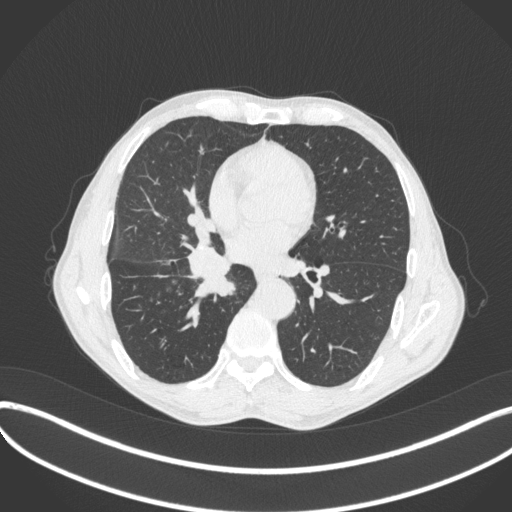
Chest CT, one axial slice. Slice 204 of 481 in the series (ordered by position). Reconstruction kernel B31f. 120 kVp. Lung window (W 1500 / L -600 HU). 1 mm slice thickness. 512 × 512 image matrix, field of view 400 × 400 mm. Patient: male, 65 years. Case-level facts recorded for this patient, not image findings: clinical TNM (as recorded): T2a N0 M0; histopathological grade: G2.
Structures marked on this image (rectangle marked by the reading radiologist):
- lung tumour (recorded histology: squamous cell carcinoma): bounding box [x1, y1, x2, y2] px = [183, 245, 237, 300]